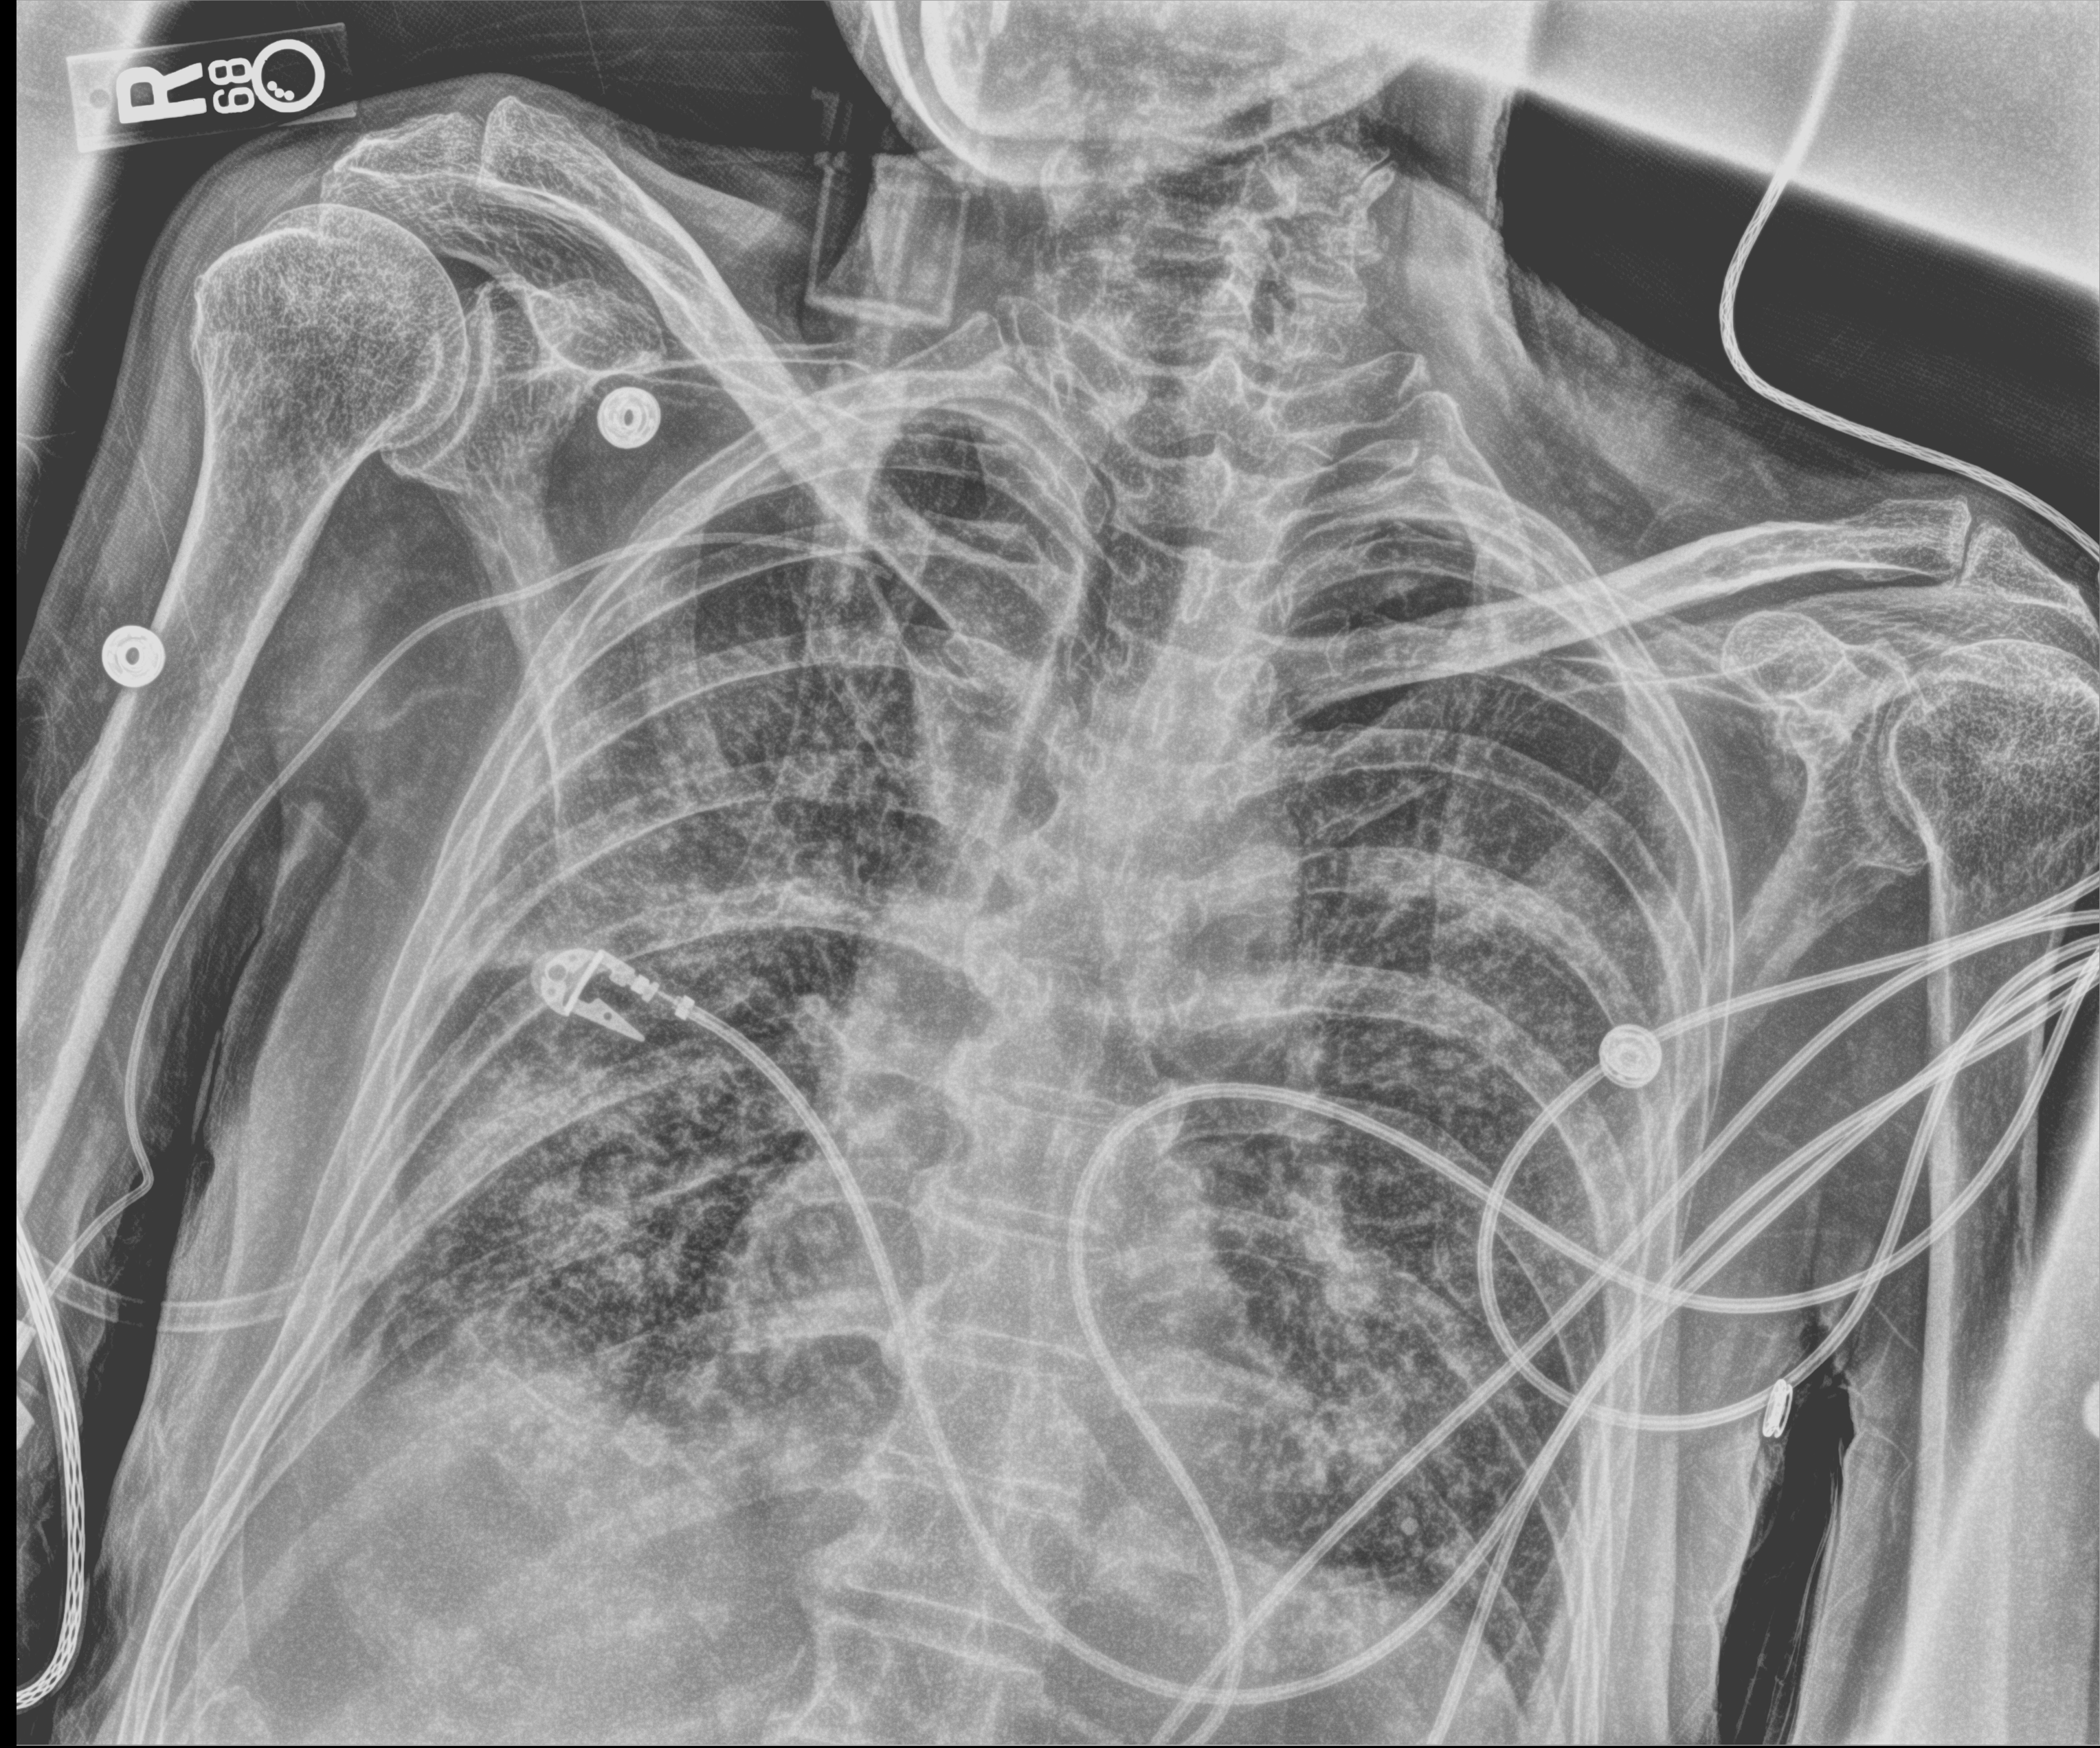
Portable chest radiograph, anteroposterior (AP) projection. Male patient hospitalised with COVID-19, age 60–74 years.
Admission-level facts for this patient (not findings on this image; timing relative to this image not recorded): diabetes (admission record): yes.